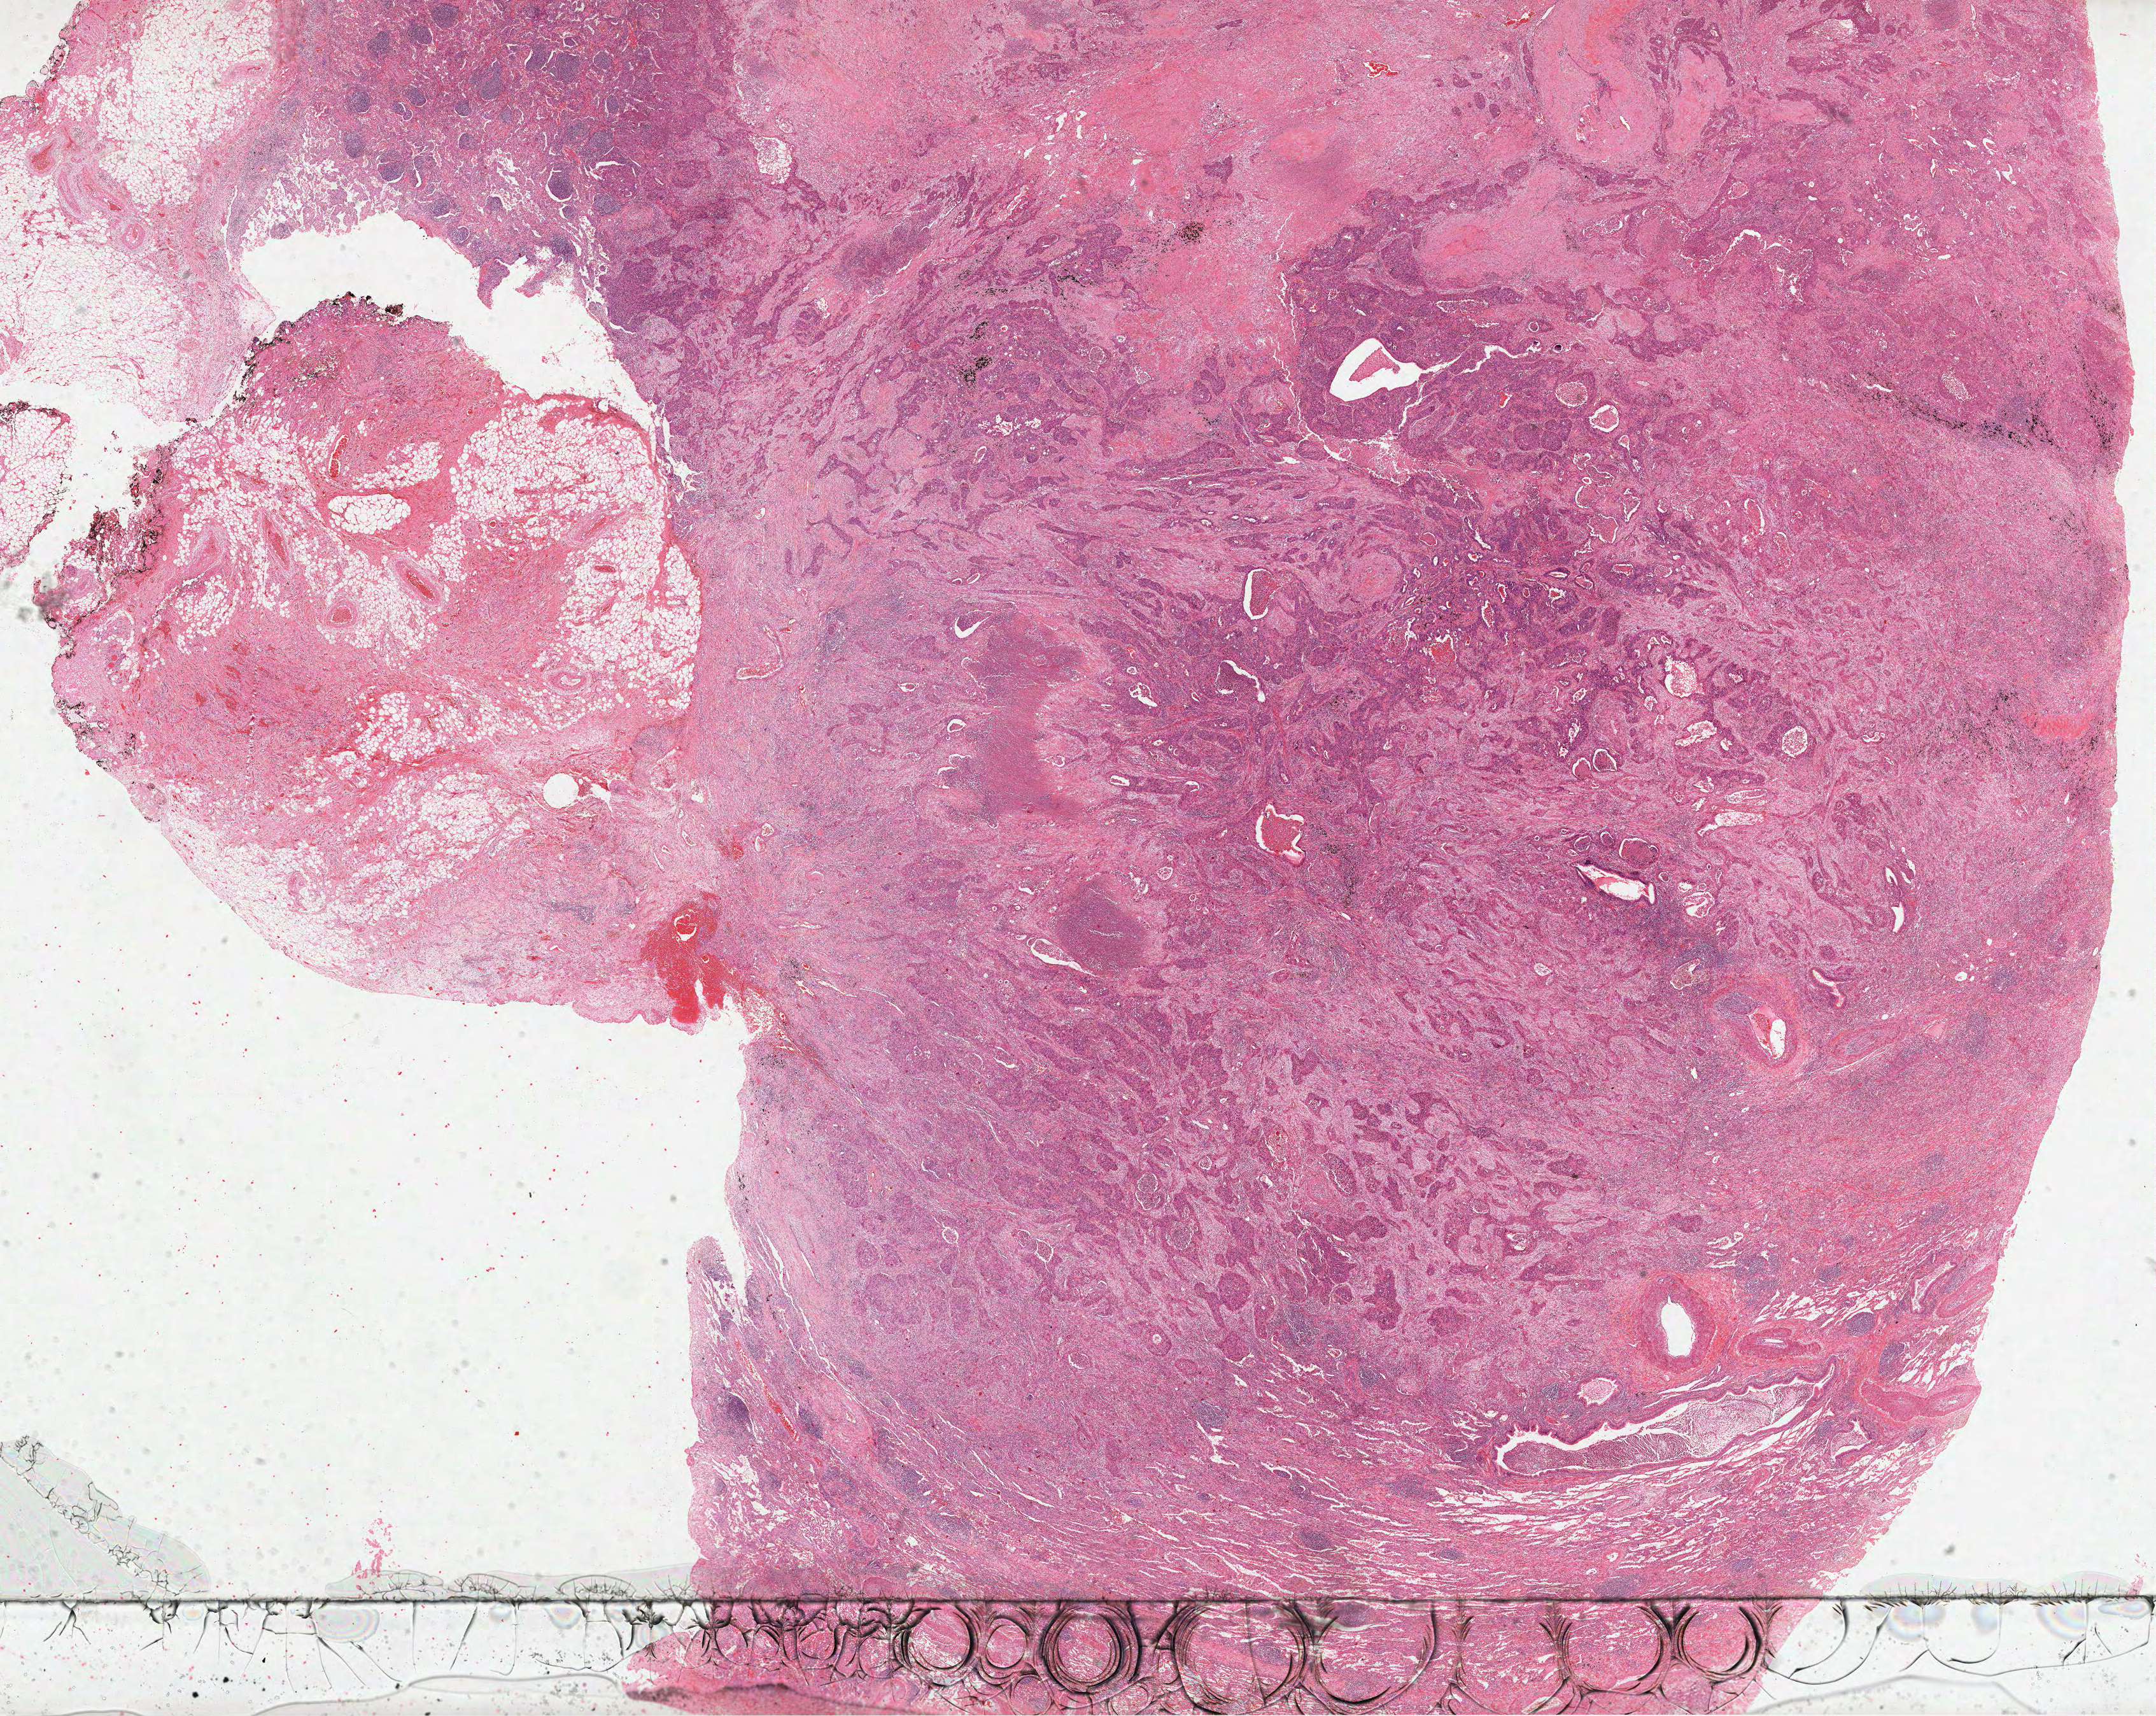
Whole-slide histology image, H&E — low-resolution overview of the scanned area, about 27.3 x 21.7 mm (slide scanned at 40x); FFPE section; primary tumour sample from the lung. Patient: male, age at initial diagnosis 74 years.
• AJCC pathologic stage: IB (6th edition)
• diagnosis: Squamous cell carcinoma, NOS
• laterality: left